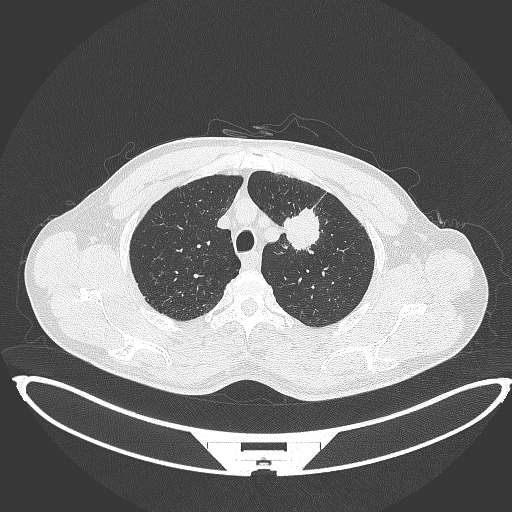
Chest CT, one axial slice; position 355 of 395 along the scan axis; reconstruction kernel B70f; 120 kVp; lung window (W 1500 / L -600 HU); 1 mm slice thickness; 512 × 512 image matrix, field of view 457 × 457 mm. Male patient, age 60 years. From the clinical record (not read from this slice): clinical TNM (as recorded): T2a N0 M0.
Structures marked on this image (bounding box drawn by a radiologist):
- lung tumour (recorded histology: squamous cell carcinoma): bounding box [x1, y1, x2, y2] px = [280, 204, 320, 252]